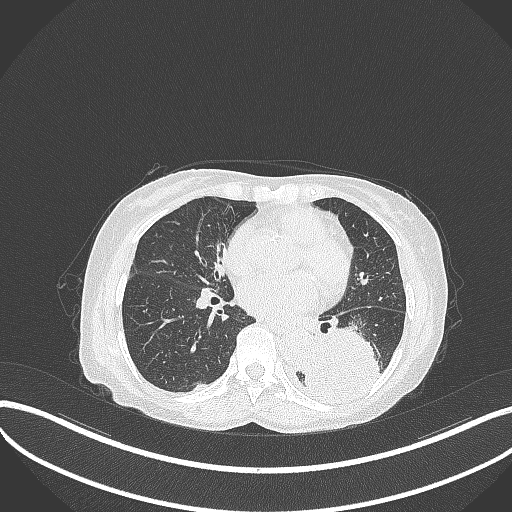
Chest CT, one axial slice. Slice 139 of 370 in the series (ordered by position). 120 kVp. Lung window (W 1500 / L -600 HU). 1 mm slice thickness. 512 × 512 image matrix, field of view 400 × 400 mm. Patient: female, 78 years. Case-level facts recorded for this patient, not image findings: clinical TNM (as recorded): T3 N0 M1.
Annotated regions visible in this slice (bounding box drawn by a radiologist):
- lung tumour (recorded histology: squamous cell carcinoma): bounding box (x1, y1, x2, y2) in pixels: (306, 321, 386, 408)